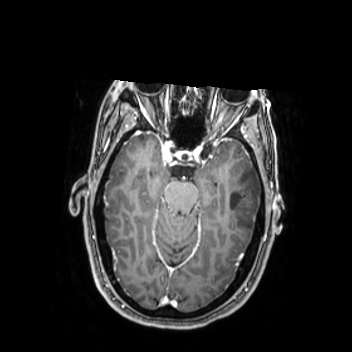
Brain MRI from a brain-tumour surgery series, one axial slice. Position 165 of 350 along the scan axis. T1-weighted post-contrast. 0.9 mm slice thickness. 352 × 352 image matrix. From the clinical record (not read from this slice): histopathology: Oligodendroglioma; WHO grade: 2; IDH mutation: yes; tumour location: Left Middle Temporal Gyrus.
Outlined on this slice (manually delineated by an expert):
- tumour: box from (x=224, y=163) to (x=262, y=236) px